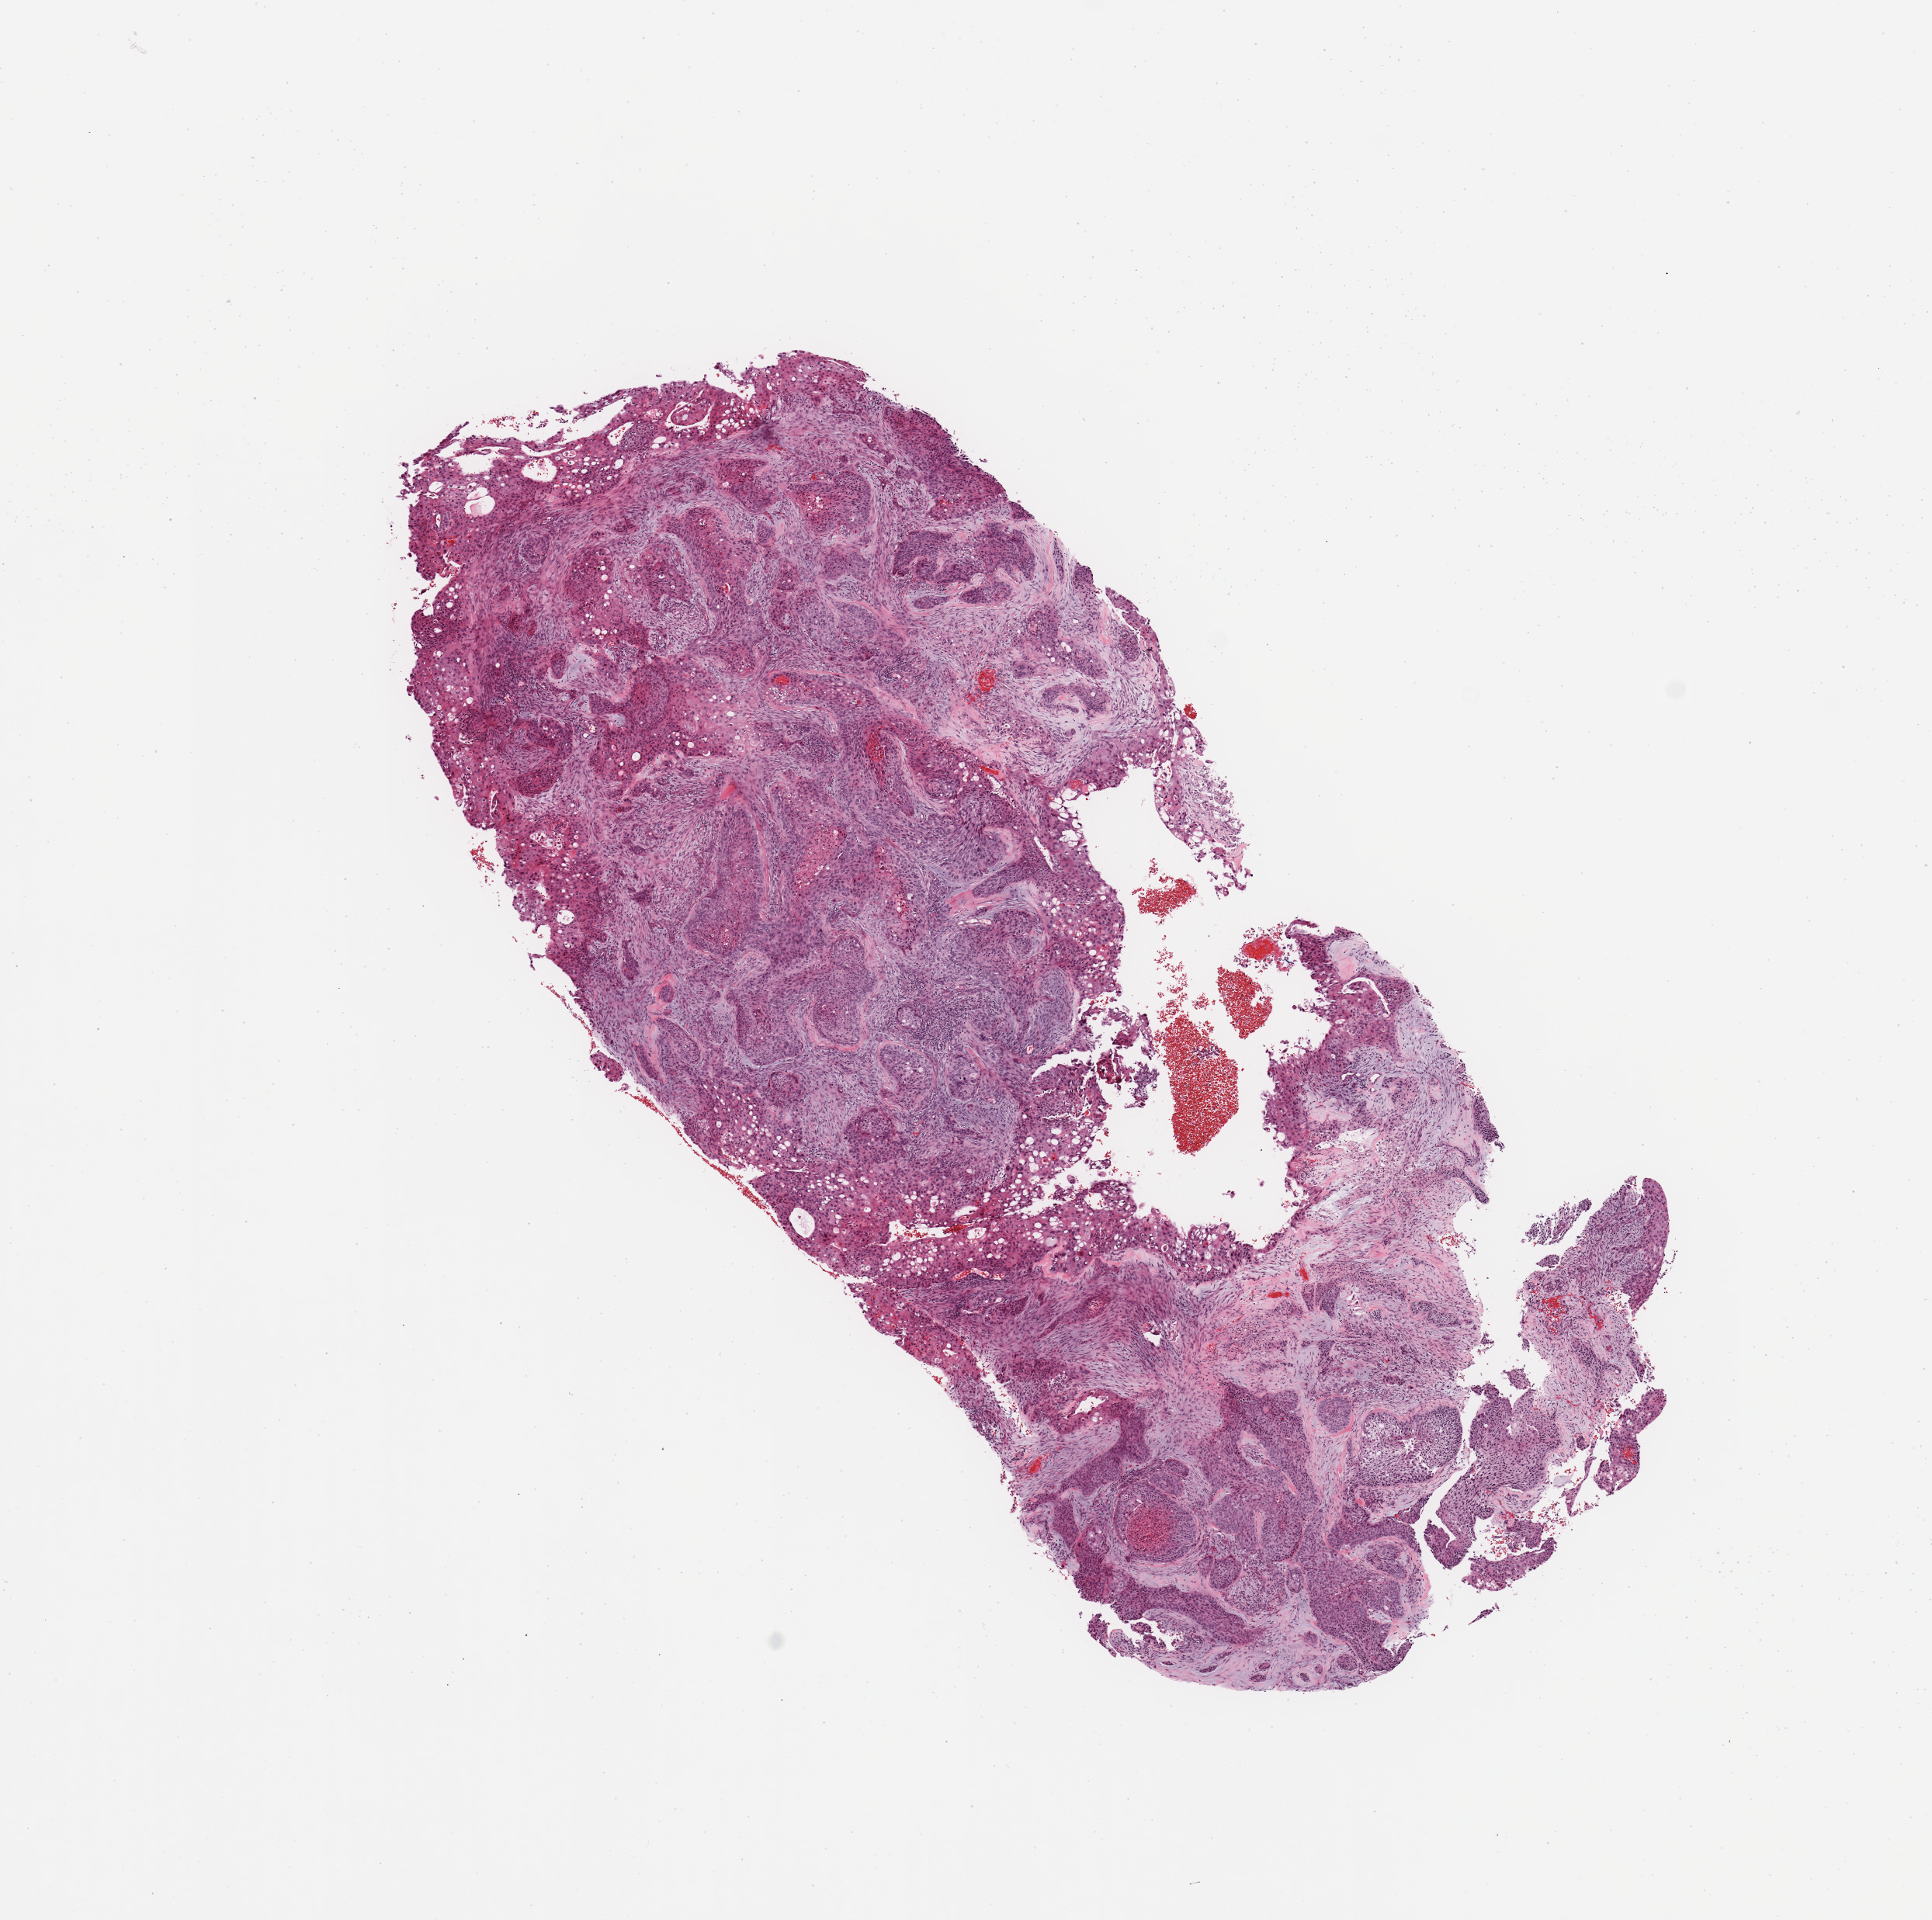
Digitized Hematoxylin and eosin (H&E) stained tissue section (whole slide), low-resolution overview of the scanned area, about 9.8 x 9.8 mm (from a 20x scan). Tumour tissue sample, sampled site: lung. Patient: male, age 74 years. Histologic grade: G2 (moderately differentiated). Slide review estimates, as recorded: tumour nuclei 80%, necrosis 2%.
Diagnosis: Squamous cell carcinoma, NOS. AJCC pathologic stage: IB. Primary tumour site (as recorded): left upper lobe.